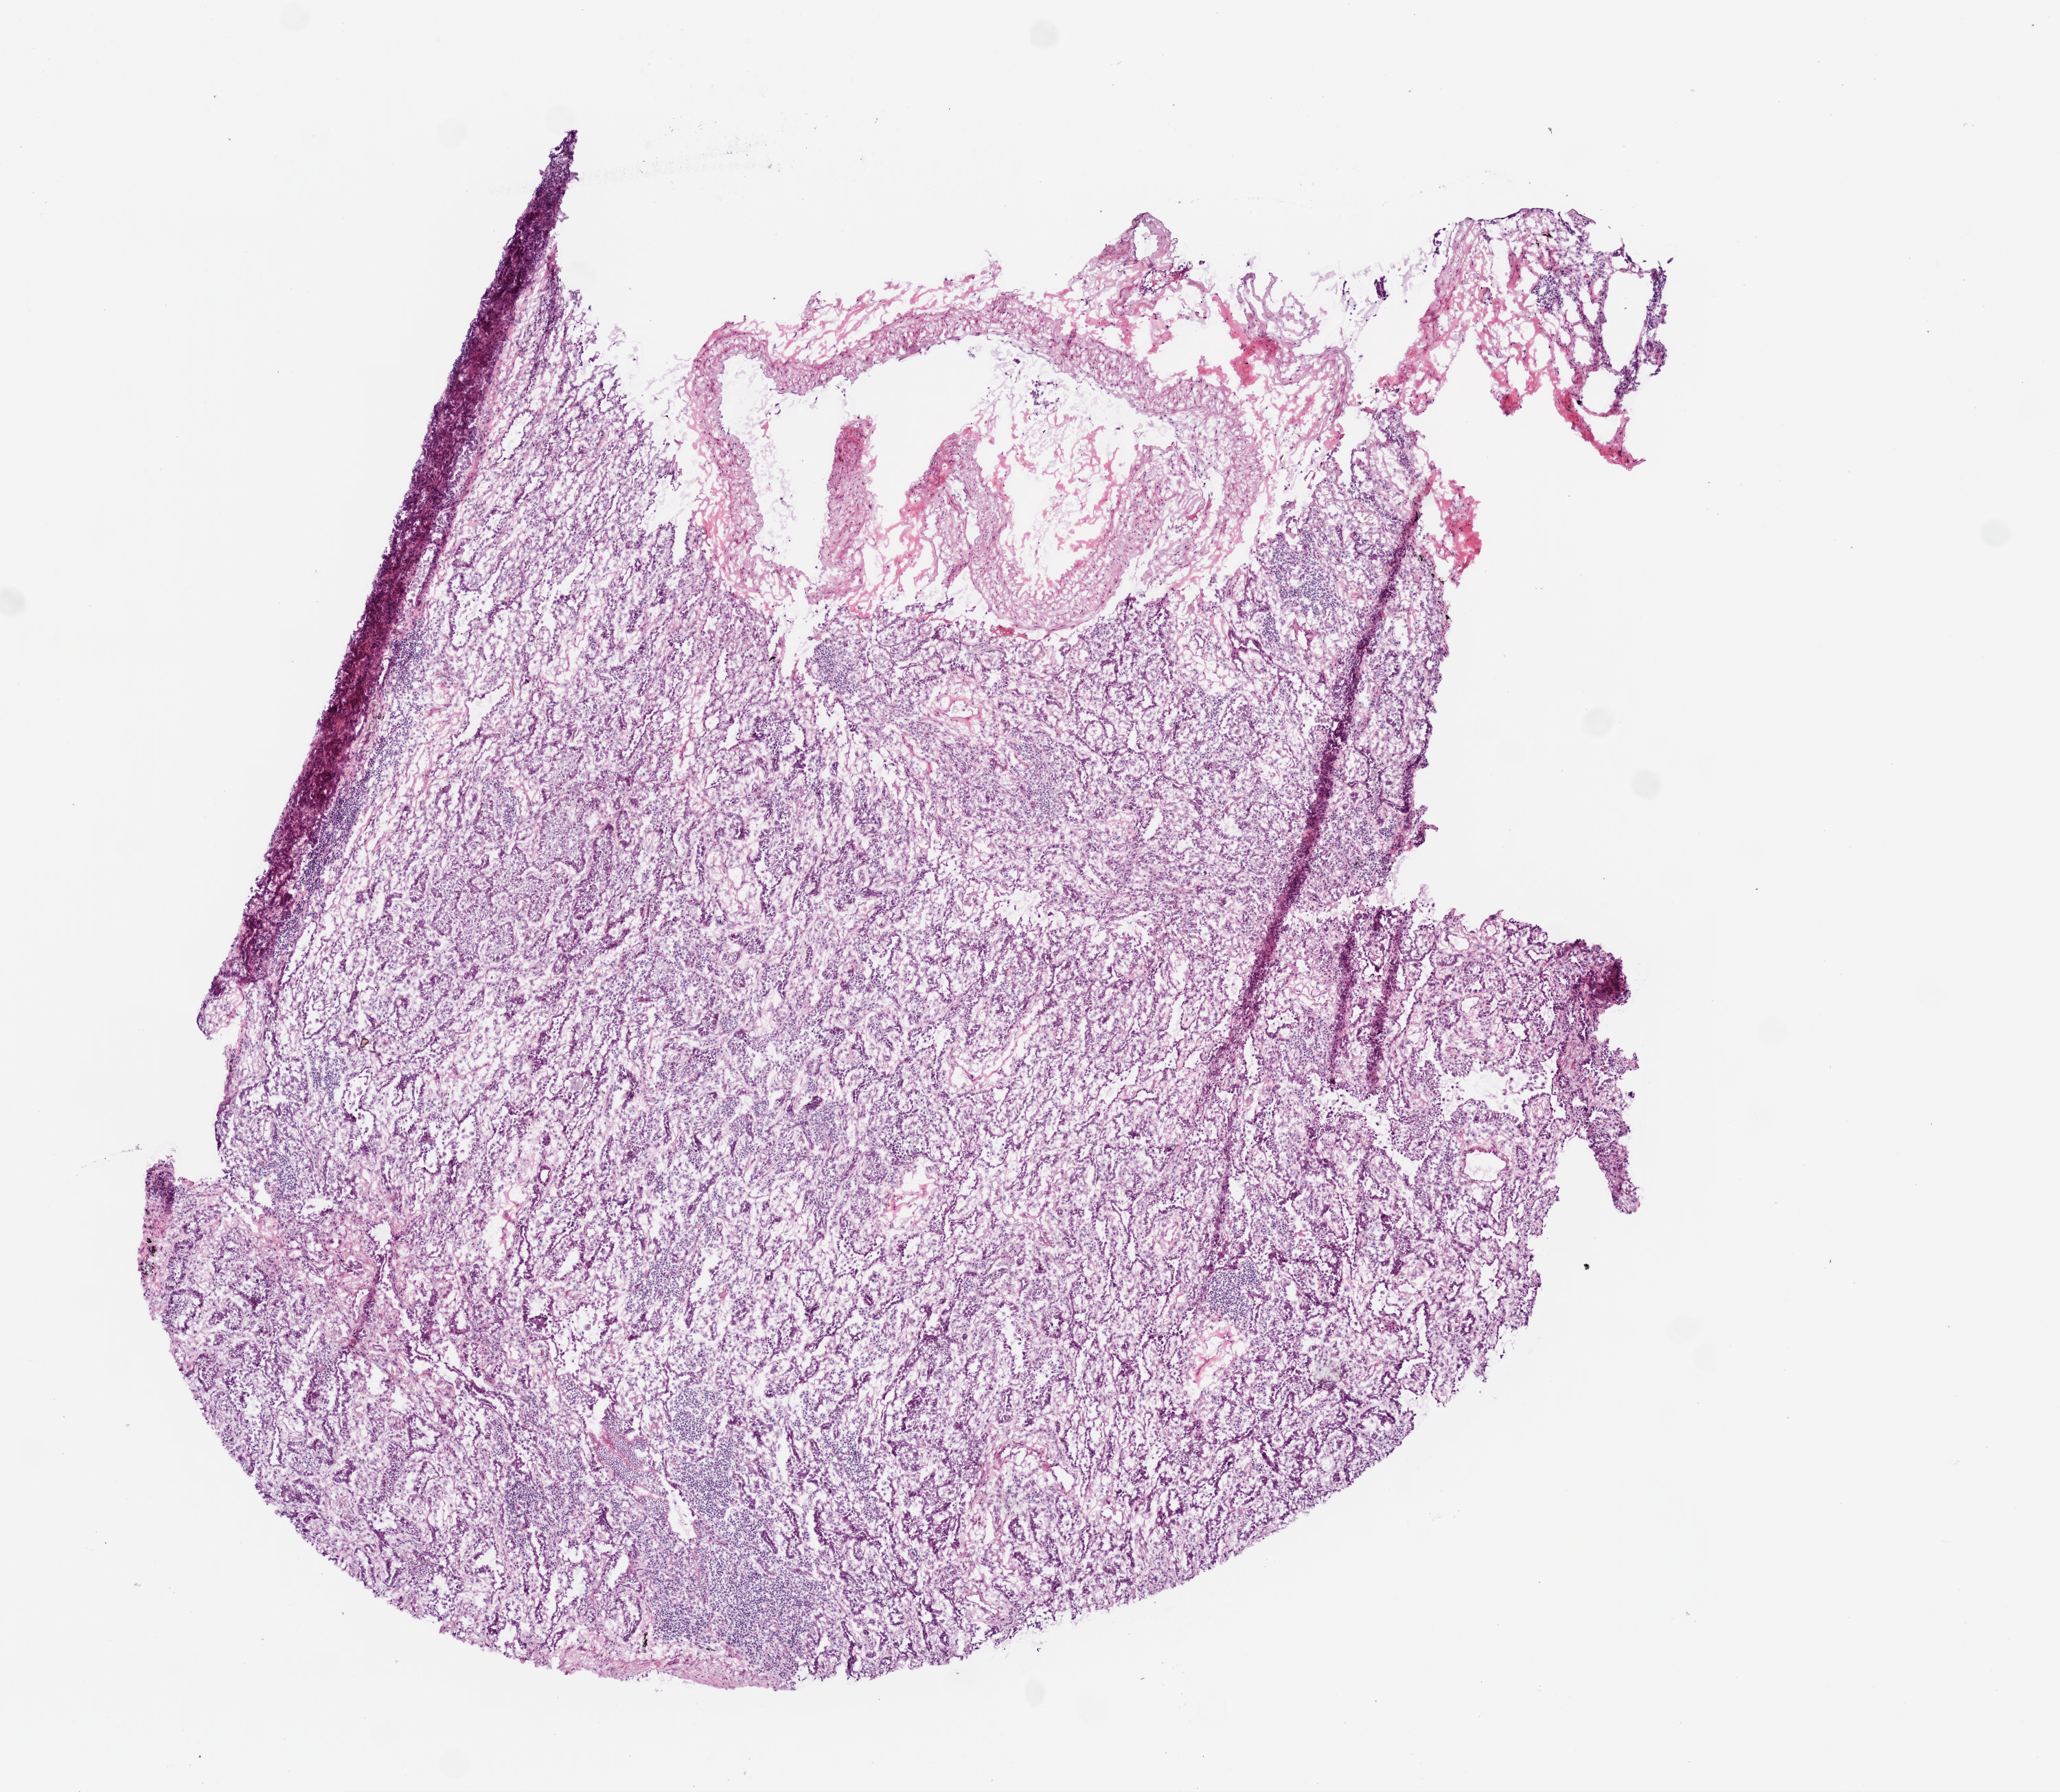
Whole-slide histology image, H&E, a low-resolution overview of the entire scanned area, about 6.0 x 5.2 mm (slide scanned at 20x), frozen section, lung, primary tumour sample. Patient sex: male. Composition of this section per pathologist review: tumour cells 95%, tumour nuclei 80%, normal cells 0%, stromal cells 5%, necrosis 0%.
Histologic diagnosis: Bronchiolo-alveolar carcinoma, non-mucinous (lower lobe, lung). AJCC pathologic stage: IB (6th edition).